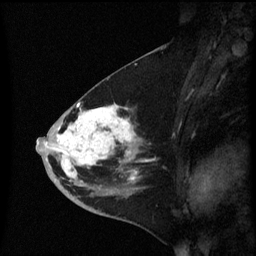
Breast MRI (dynamic contrast-enhanced), one sagittal slice. Position 29 of 60 along the scan axis. Dynamic contrast-enhanced series, image 2 of 3 at this slice position (ordered by acquisition). 1.5 T. TE 4.2 ms, TR 8.4 ms. 2.3 mm slice thickness. 256 × 256 image matrix, field of view 200 × 200 mm. Patient: female, 46 years. From the clinical record (not read from this slice): setting: breast cancer imaged before/during neoadjuvant chemotherapy; receptor status: HER2-positive.
Annotated regions visible in this slice (semi-automatic segmentation, software-assisted and operator-edited):
- analysis volume of interest (the breast-tissue region the enhancement analysis was run in; not a lesion): bounding box <36,96,144,187> (left, top, right, bottom; pixels)
- tumour enhancement mask (voxels above the 70 % enhancement threshold inside the analysis volume of interest): <37,102,137,181>